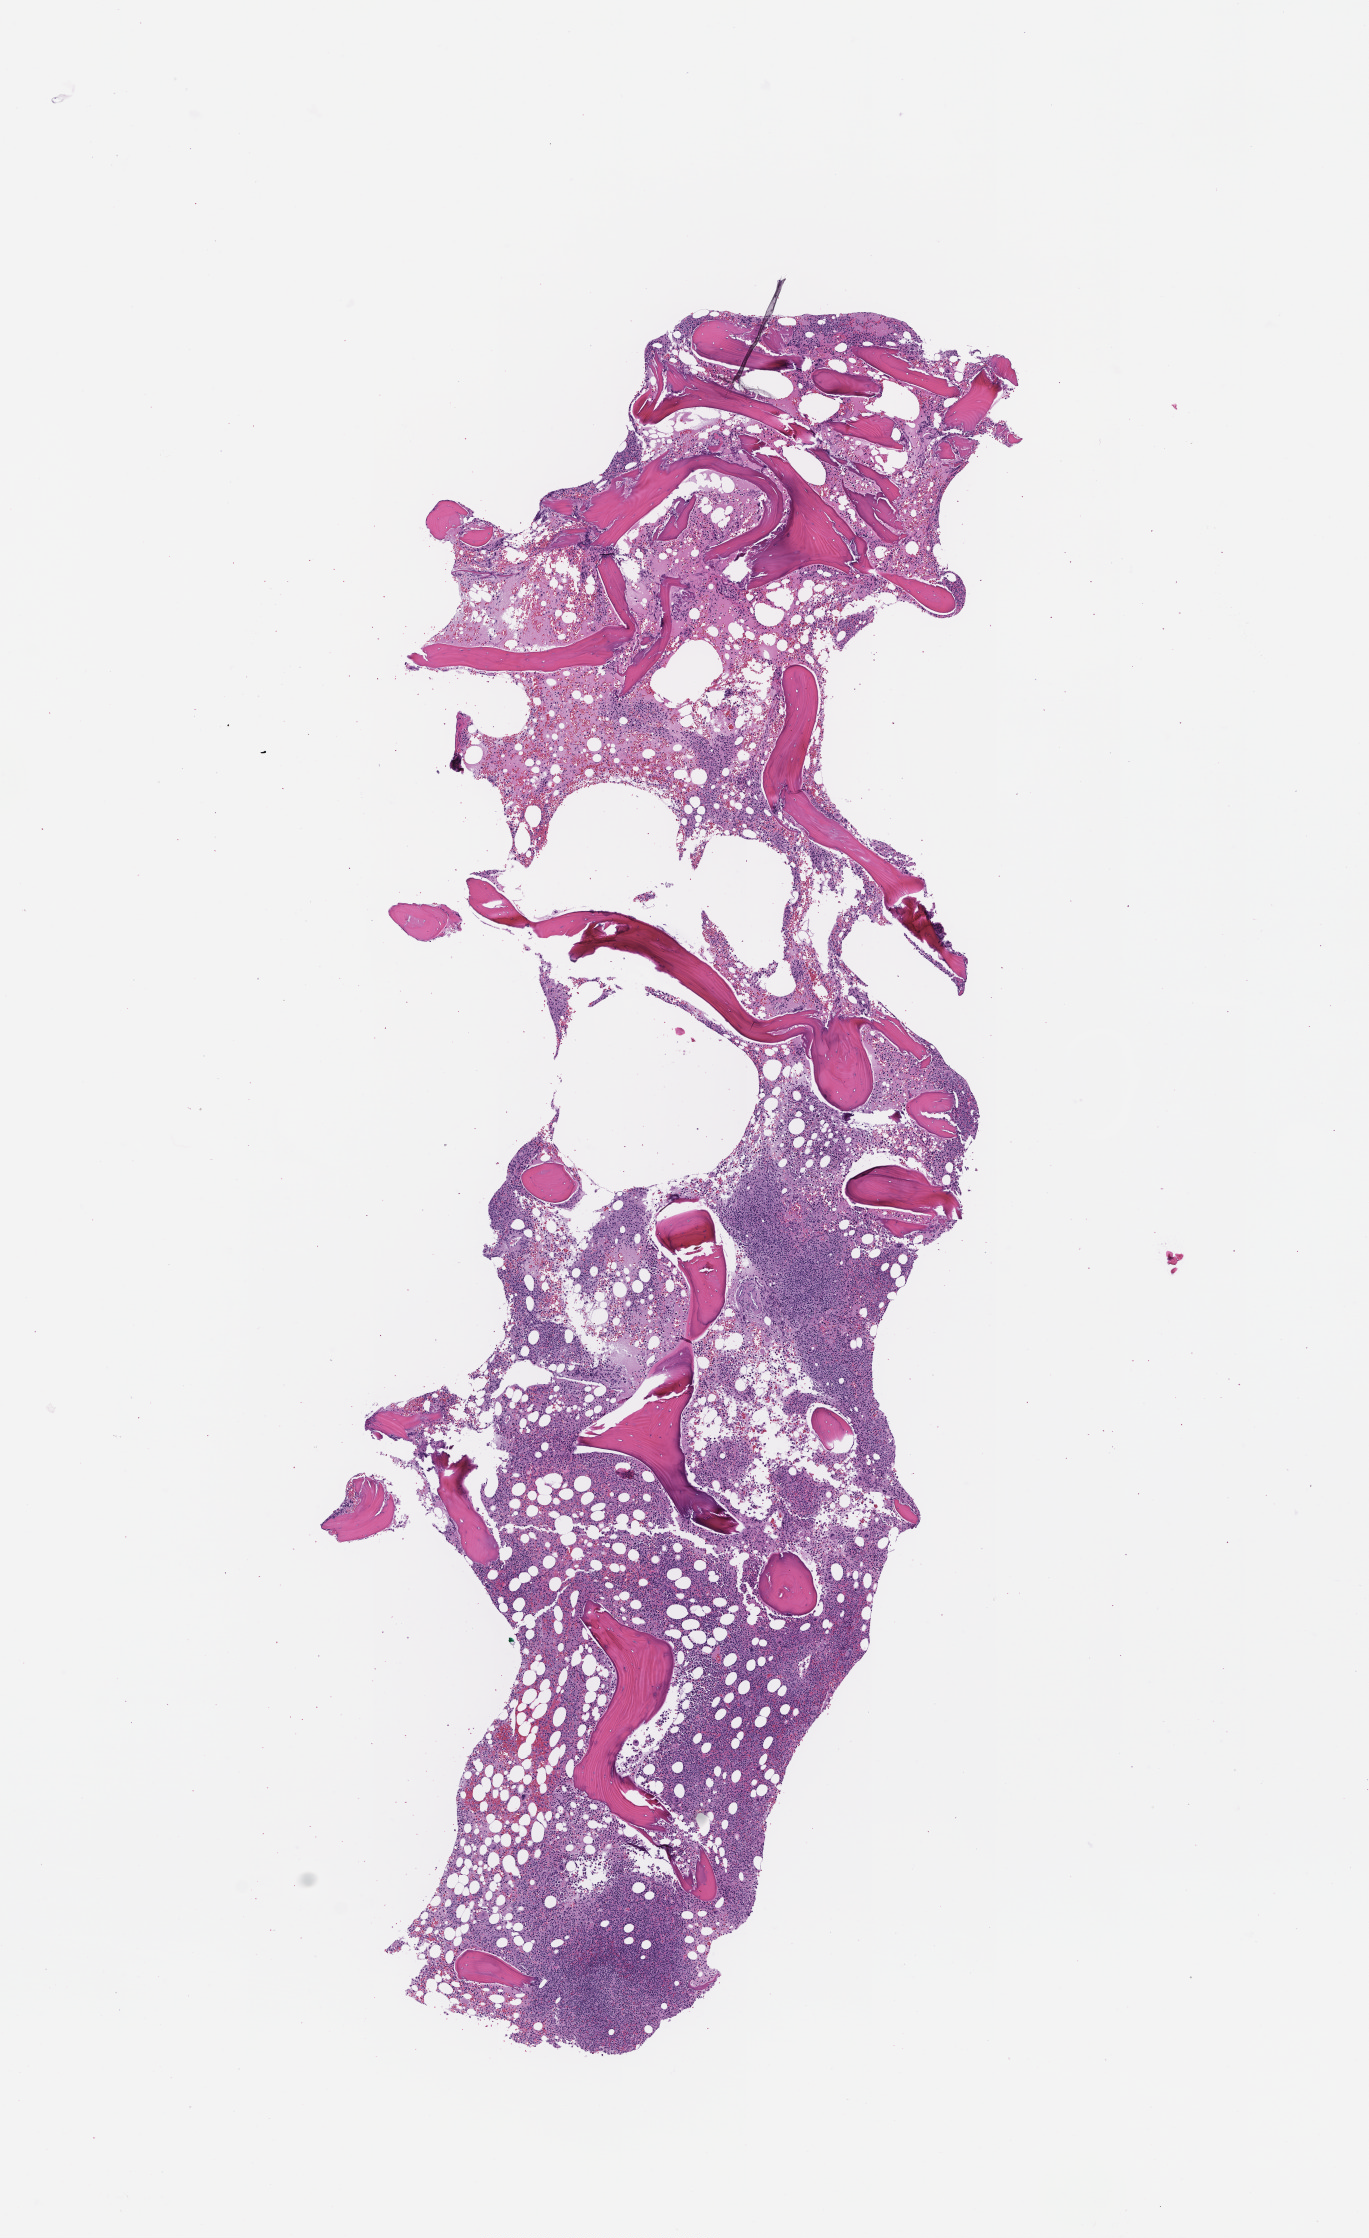
Digitized hematoxylin and eosin (H&E)-stained section — low-resolution overview of the scanned area, about 5.5 x 9.0 mm, FFPE section, tissue site: bone marrow, specimen time point: archival tissue. Patient: female.
This section: primary tumour tissue. Diagnosis: Plasma Cell Myeloma.